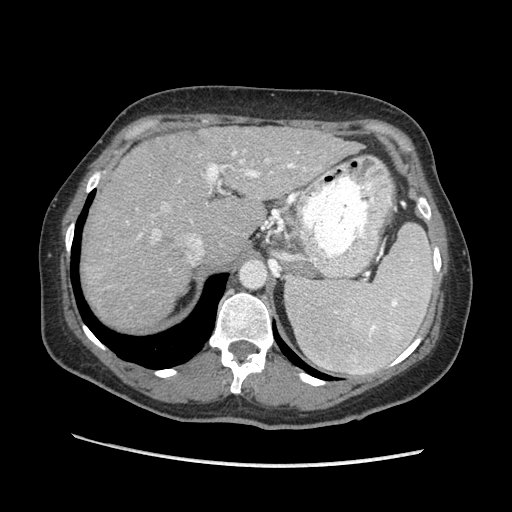
Contrast-enhanced abdominal CT (liver protocol), one axial slice. Position 141 of 170 along the scan axis. Reconstruction kernel STANDARD. 140 kVp. Soft-tissue window (W 400 / L 40 HU). 512 × 512 image matrix, field of view 360 × 360 mm. From the clinical record (not read from this slice): diagnosis: hepatocellular carcinoma (patient treated with transarterial chemoembolisation; whether this scan precedes or follows treatment is not stated here); TNM stage (as recorded): Stage-II; Child-Pugh class: A; tumour differentiation: no biopsy.
Annotated regions visible in this slice (semi-automatically segmented with operator editing):
- abdominal aorta: bounding box <241,263,265,287> (left, top, right, bottom; pixels)
- liver parenchyma outside the tumour (the mass and vessels are separate outlines, so this box may not span the whole liver): <82,126,361,330>
- liver vessels: <139,150,306,264>